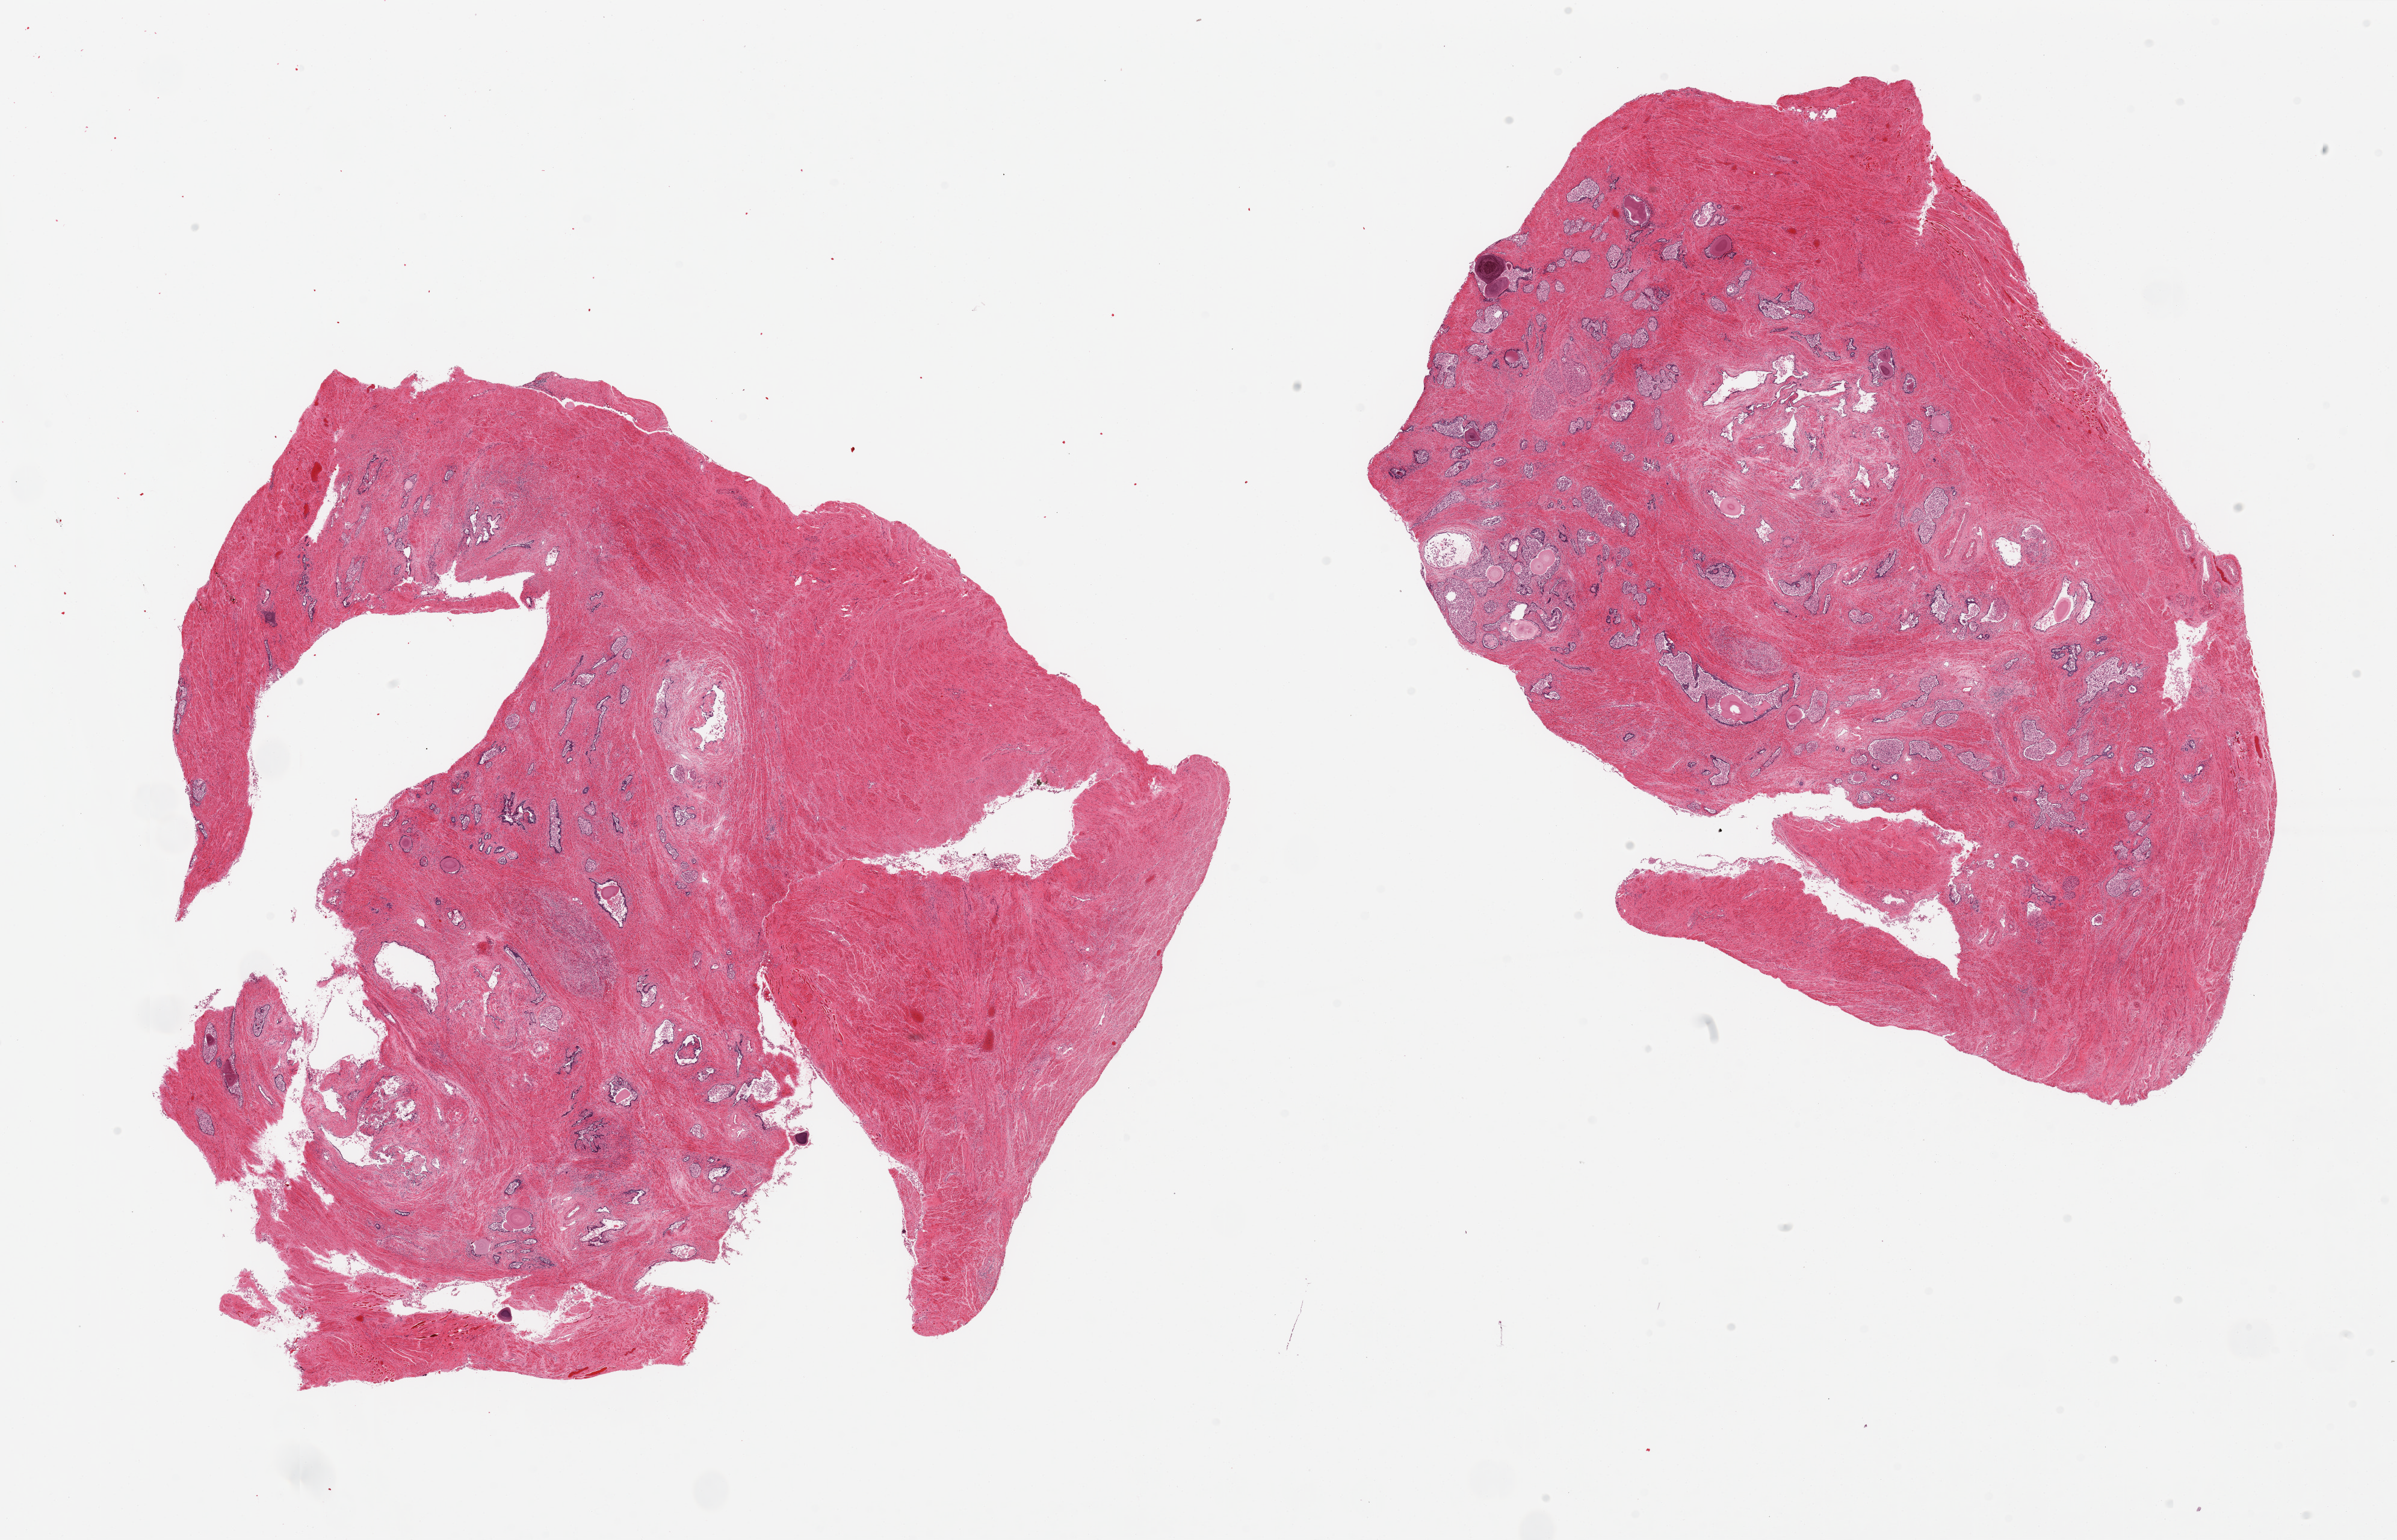
Digitized hematoxylin and eosin (H&E)-stained section — whole scanned area (about 31.5 x 20.2 mm) shown as a low-resolution overview, PAXgene-fixed, paraffin-embedded tissue, sampled site (target tissue): prostate, donor tissue sample.
Reviewer comment on this tissue sample: 2 pieces; glands largely autolyzed, fibromuscular stroma slightly autolyzed.